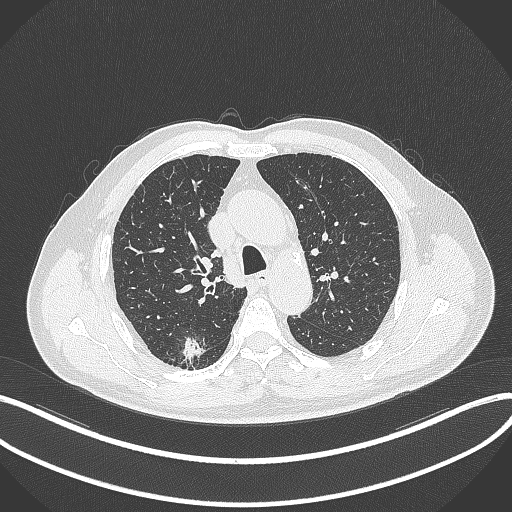
Chest CT, one axial slice; position 261 of 359 along the scan axis; 120 kVp; lung window (W 1500 / L -600 HU); 1 mm slice thickness; 512 × 512 image matrix, field of view 400 × 400 mm. Male patient, age 69 years. Case-level facts recorded for this patient, not image findings: clinical TNM (as recorded): T1b N0 M0.
Outlined on this slice (bounding box drawn by a radiologist):
- lung tumour (recorded histology: adenocarcinoma): box from (x=181, y=332) to (x=204, y=366) px